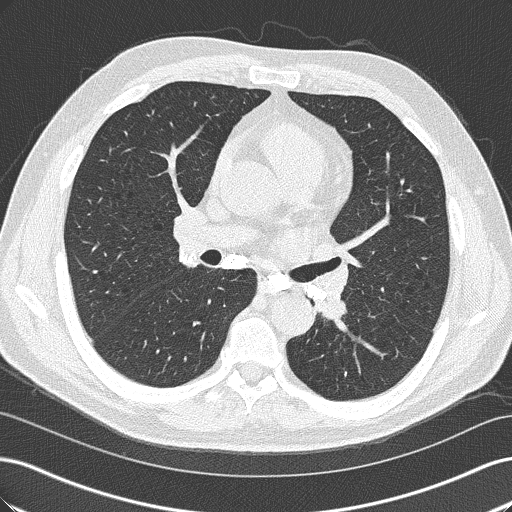
Axial slice from a low-dose chest CT screening exam; first (baseline) screen; lung window (W 1500 / L -600 HU); 2 mm slice thickness; lung (sharp) reconstruction kernel (B50f); slice 78 of 152 in the series; 512 × 512 image matrix, field of view 360 × 360 mm. Male participant, aged 57 years at enrolment. Former smoker at enrolment.
- Expert-annotated lung lesion, bounding box [x1, y1, x2, y2] px = [302, 284, 361, 341].
- No non-calcified nodule or mass ≥4 mm was recorded by the screening reader at this exam.
- Lung cancer was diagnosed 363 days after this screen (after the second annual screen): squamous cell carcinoma, NOS, left lower lobe, moderately differentiated (G2), stage IIIB (AJCC 6th edition), 38 mm at pathology.